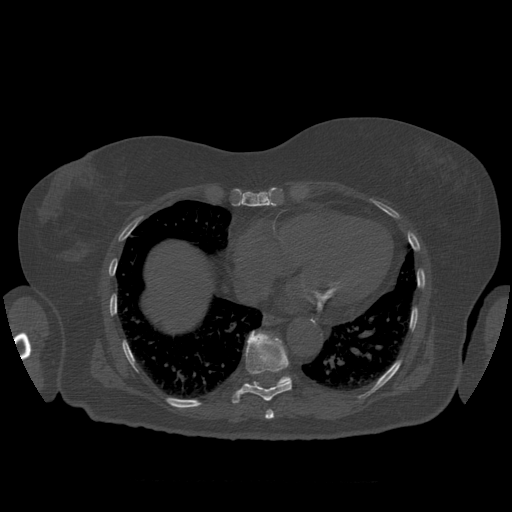
CT including the spine, one axial slice. Slice 356 of 399 in the series (ordered by position). 120 kVp. Bone window (W 1800 / L 400 HU). 1.25 mm slice thickness. 512 × 512 image matrix, field of view 404 × 404 mm. Patient age 81 years. Case-level facts recorded for this patient, not image findings: primary cancer: renal.
Annotated regions visible in this slice (semi-automatically segmented with operator editing):
- T10 vertebra: box from (x=248, y=341) to (x=292, y=388) px
- T8 vertebra: (x=265, y=410)–(x=274, y=420)
- T9 vertebra: (x=232, y=331)–(x=292, y=404)